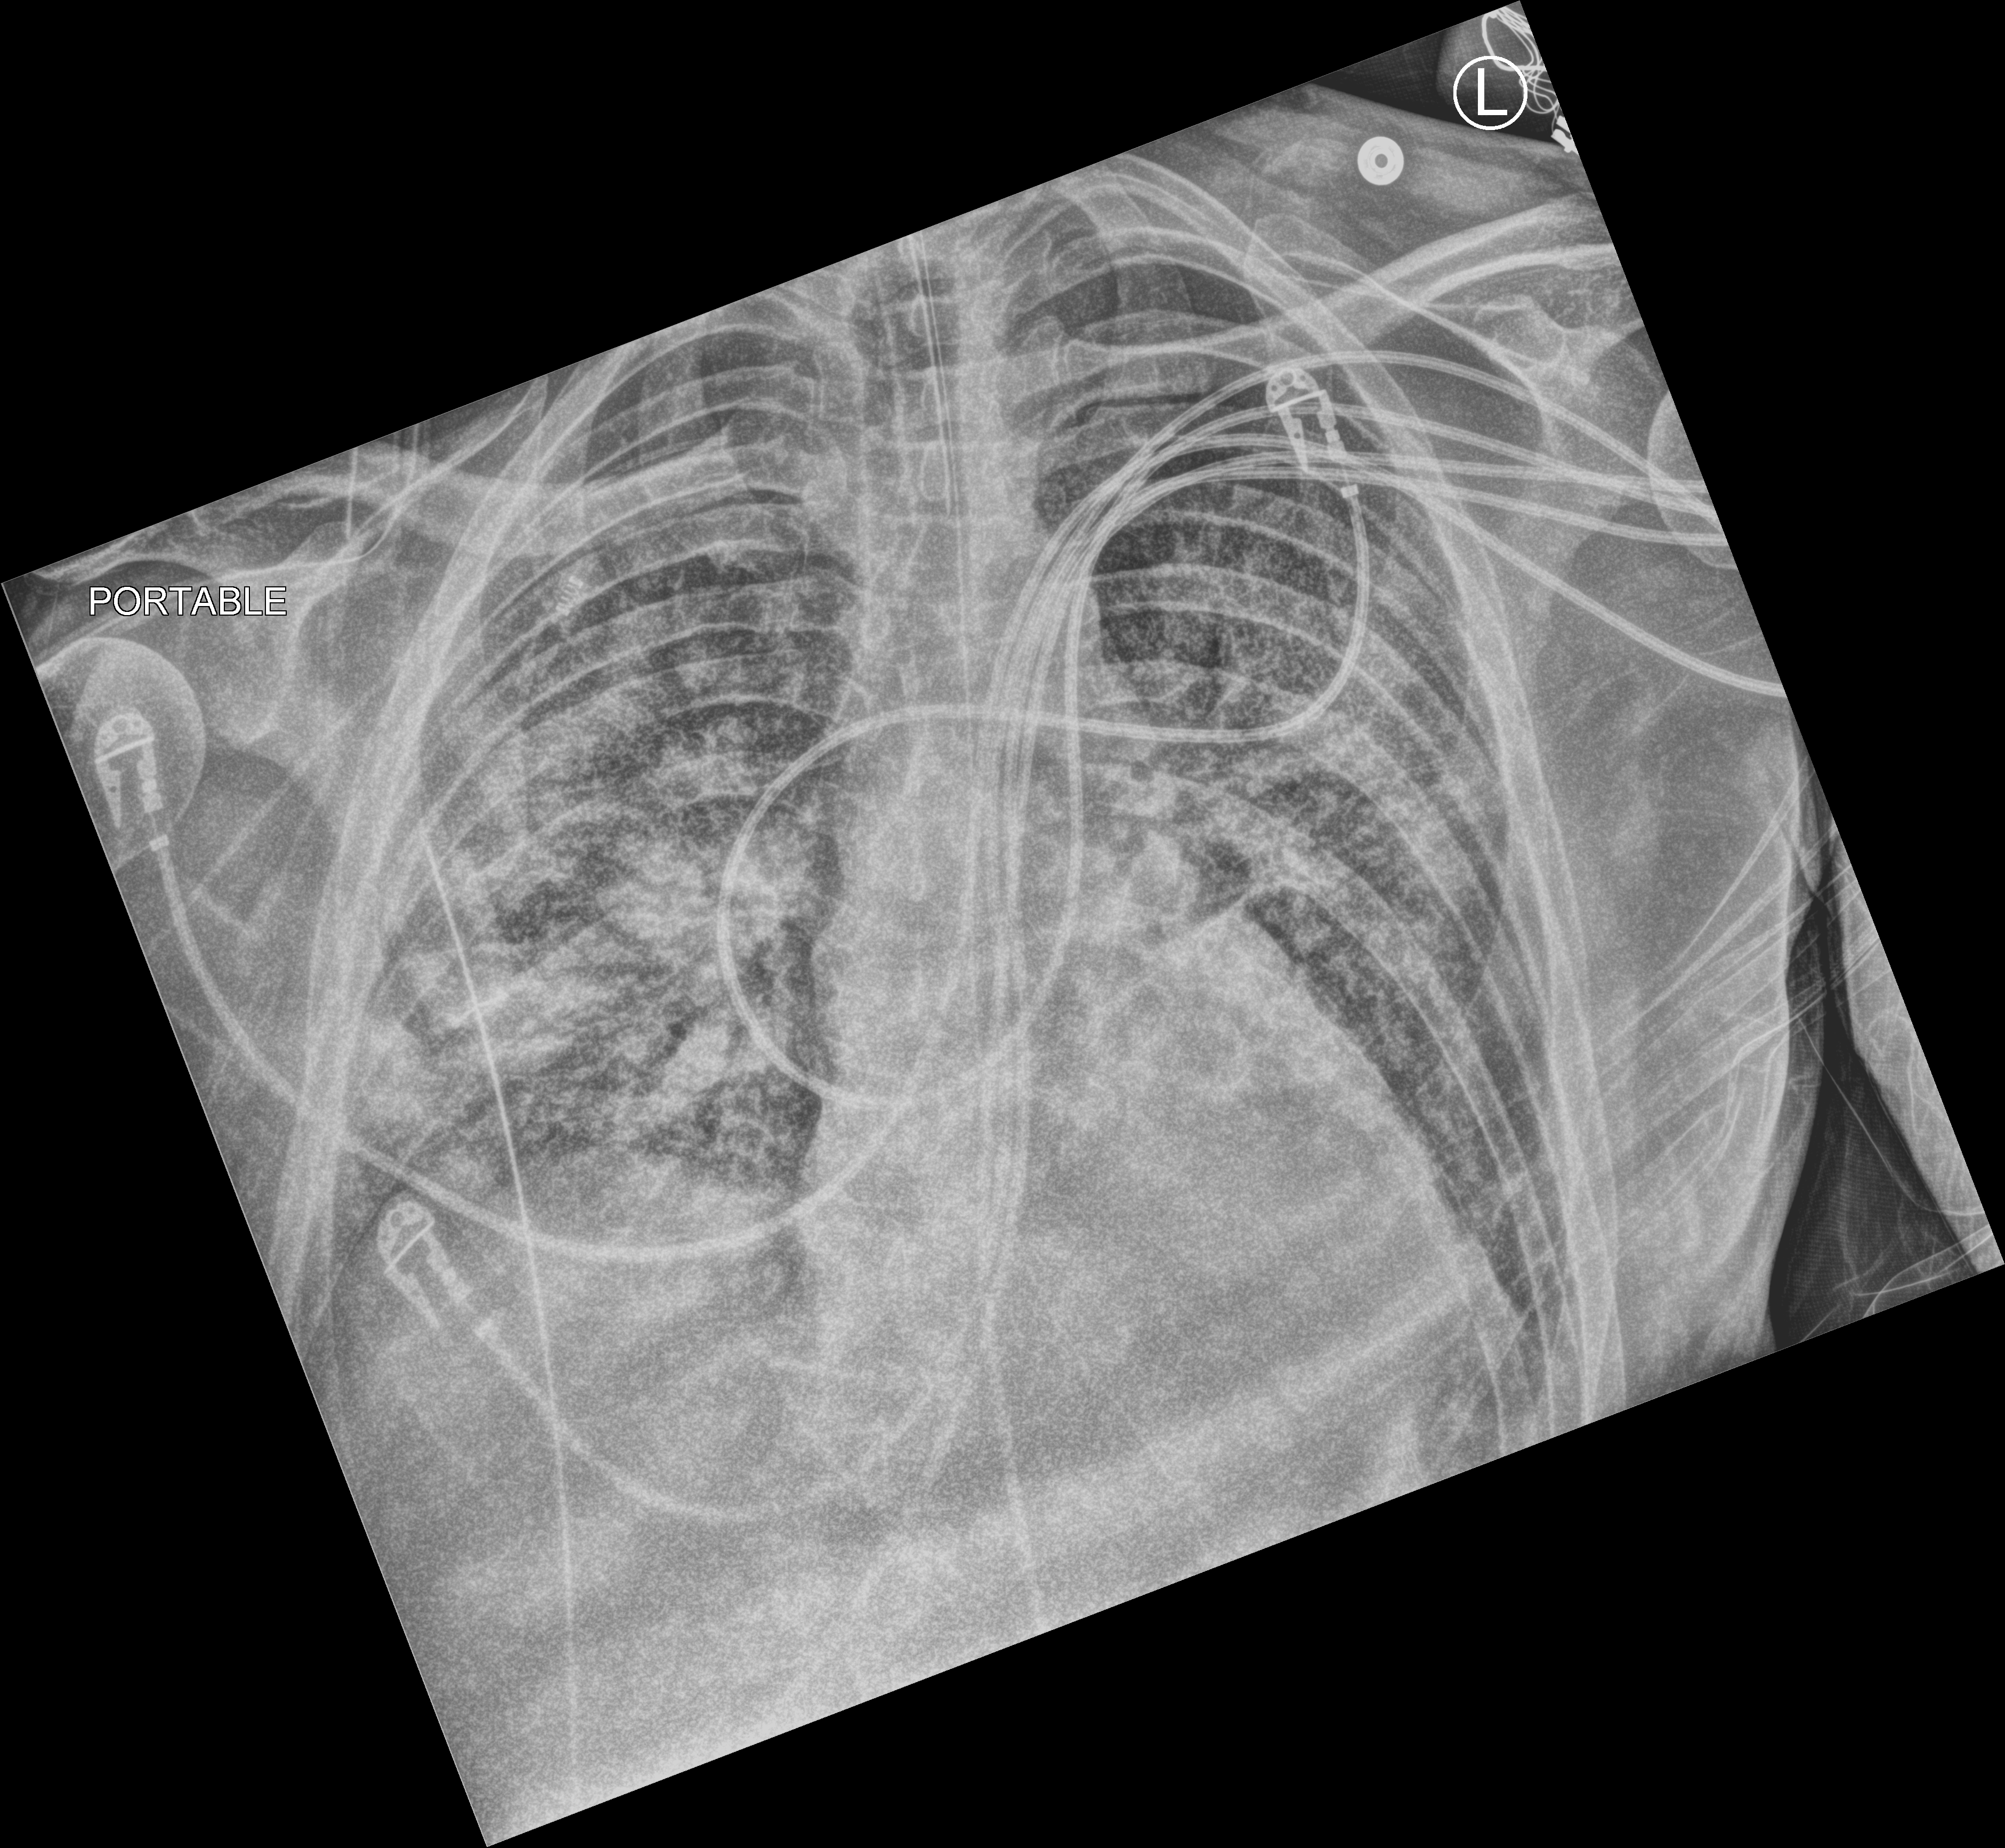
Portable chest radiograph, anteroposterior (AP) projection. Patient hospitalised with COVID-19; male, aged 18–59 years.
Admission-level facts for this patient (not findings on this image; timing relative to this image not recorded): mechanically ventilated during this hospital stay: yes.